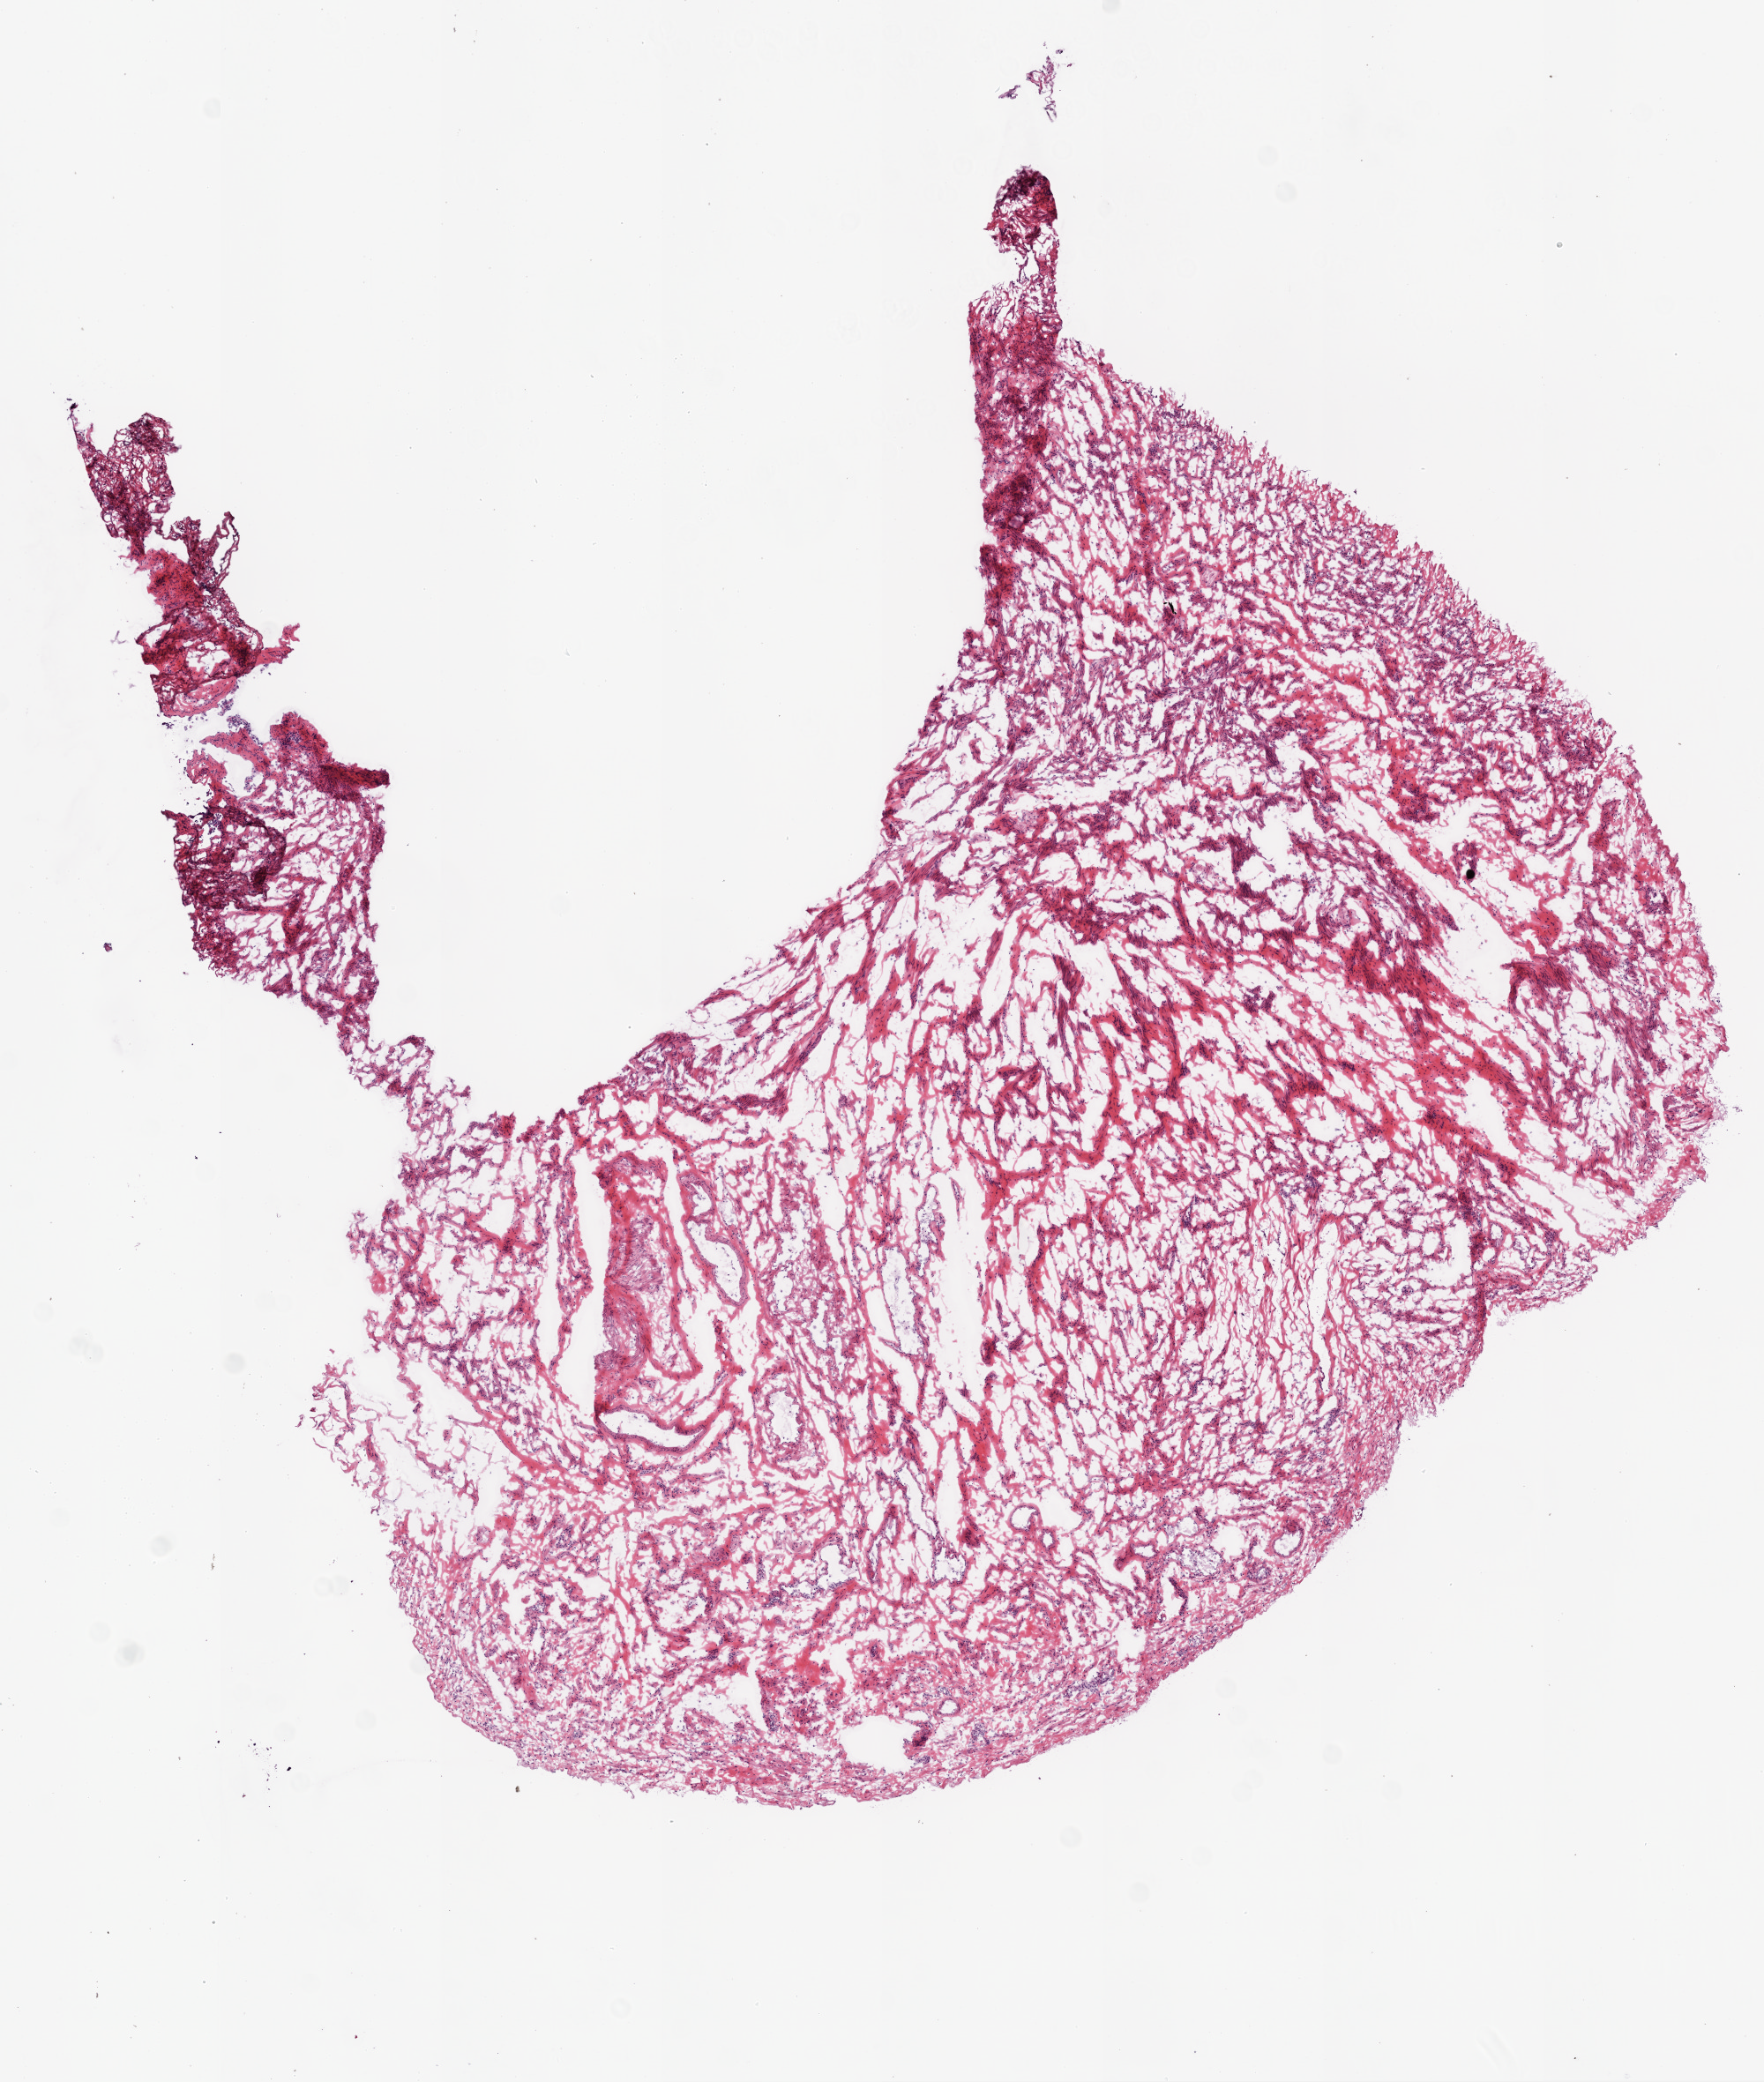
Whole-slide histology image, H&E, a low-resolution overview of the entire scanned area, about 8.0 x 9.5 mm (slide scanned at 20x); frozen section; solid tissue normal (non-tumour tissue) sample from the ovary. Female, age 55 years at initial diagnosis.
This section: solid tissue normal (non-tumour) sample from the same patient. Patient diagnosis: Serous cystadenocarcinoma, NOS.